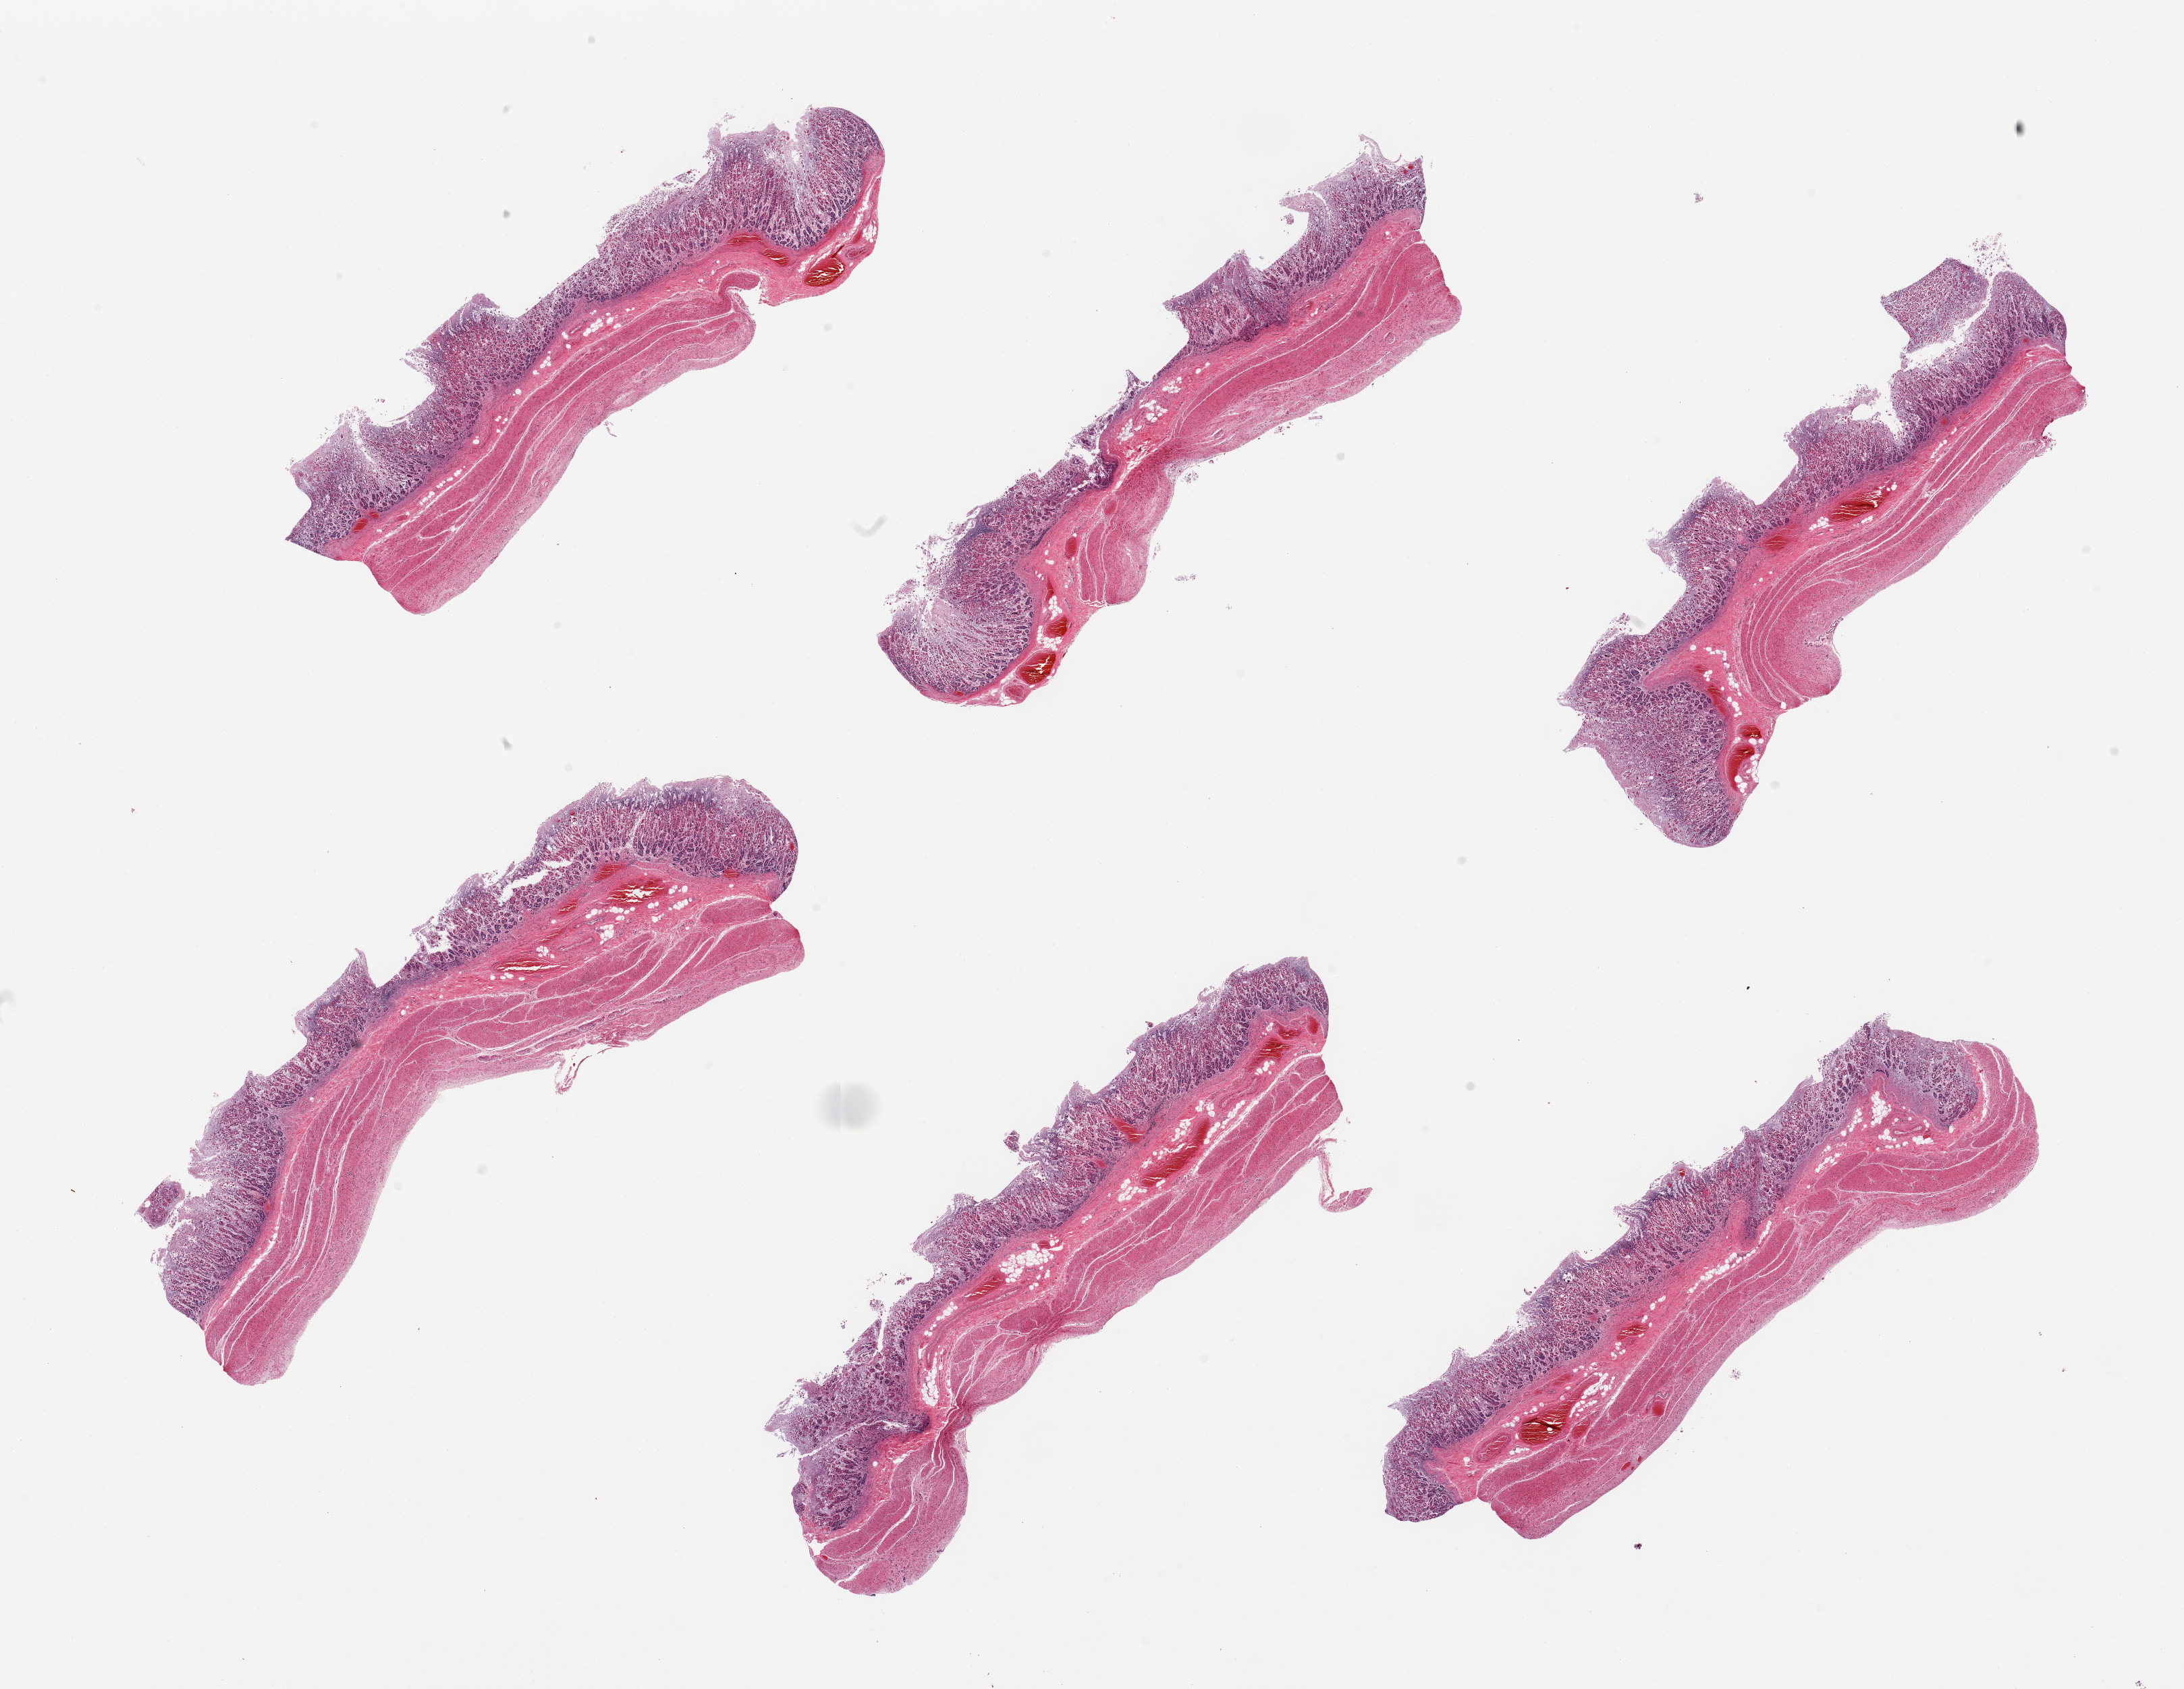
Hematoxylin and eosin (H&E) whole-slide image — shown as a low-resolution overview of the whole scanned area (about 25.6 x 19.8 mm), PAXgene-fixed paraffin-embedded (PFPE) section, target tissue: stomach, tissue donor sample. Female donor.
Pathologist's review note for this sample: 6 pieces, mucosa up to ~1mm thick, ~50% thickness but moderately to markeldy autolyzed.